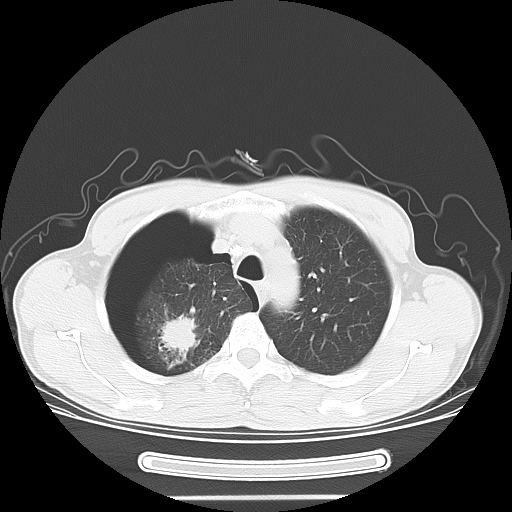
Chest CT, one axial slice; position 53 of 67 along the scan axis; 120 kVp; lung window (W 1500 / L -600 HU); 5 mm slice thickness; 512 × 512 image matrix, field of view 375 × 375 mm. Male patient. Case-level facts recorded for this patient, not image findings: clinical TNM (as recorded): T1c N0 M0.
Annotated regions visible in this slice (rectangle marked by the reading radiologist):
- lung tumour (recorded histology: adenocarcinoma): bounding box <149,305,202,362> (left, top, right, bottom; pixels)